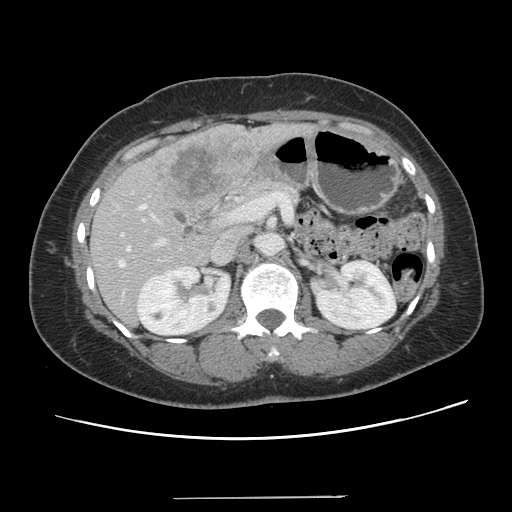
Contrast-enhanced abdominal CT, one axial slice. Position 65 of 141 along the scan axis. 120 kVp. Soft-tissue window (W 400 / L 40 HU). 2.5 mm slice thickness. 512 × 512 image matrix, field of view 366 × 366 mm. Female patient, age 53 years. Case-level facts recorded for this patient, not image findings: diagnosis: colorectal cancer liver metastases, imaged before liver resection; multiple liver metastases: no.
Structures marked on this image (outlined manually by an expert reader):
- hepatic veins: bounding box [x1, y1, x2, y2] px = [118, 246, 129, 266]
- liver: [91, 124, 303, 325]
- planned liver remnant (the part of the liver to remain after resection): [91, 212, 224, 326]
- portal vein (with intrahepatic branches): [121, 205, 164, 245]
- liver metastasis: [152, 136, 249, 203]